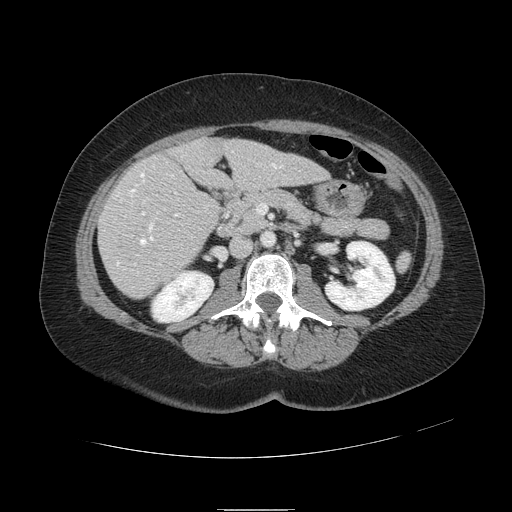
Contrast-enhanced abdominal CT, one axial slice; position 38 of 121 along the scan axis; 120 kVp; intravenous contrast given; soft-tissue window (W 400 / L 40 HU); 512 × 512 image matrix, field of view 400 × 400 mm. Female patient, age 52 years. From the clinical record (not read from this slice): diagnosis: colorectal cancer liver metastases, imaged before liver resection; multiple liver metastases: yes; largest metastasis: 6.3 cm.
Annotated regions visible in this slice (outlined manually by an expert reader):
- hepatic veins: box from (x=117, y=156) to (x=277, y=265) px
- liver: (x=99, y=138)–(x=327, y=298)
- planned liver remnant (the part of the liver to remain after resection): (x=177, y=137)–(x=328, y=190)
- portal vein (with intrahepatic branches): (x=142, y=193)–(x=178, y=217)